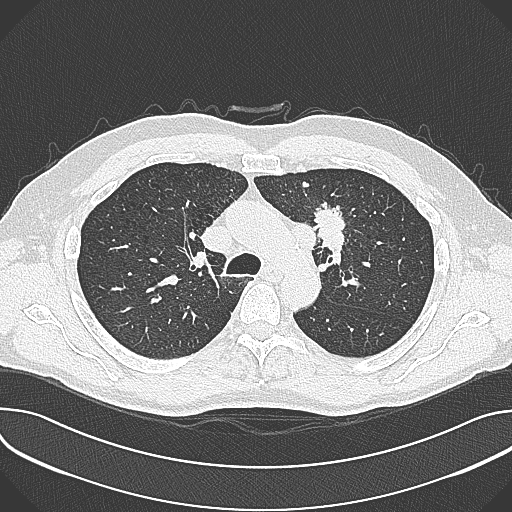
Axial slice from a low-dose chest CT screening exam. First (baseline) screen. Lung window (W 1500 / L -600 HU). 1 mm slice thickness. Male participant, aged 59 years at enrolment.
Expert reader's lesion annotation, bounding box [x1, y1, x2, y2] px = [302, 197, 361, 257]. The screening reader recorded 2 non-calcified nodules or masses ≥4 mm on this exam; which of them this box marks is not recorded. Official screen result: positive, change unspecified: nodule(s) >= 4 mm or enlarging nodule(s), mass(es), or other non-specific abnormalities suspicious for lung cancer. Later outcome: lung cancer diagnosed 21 days after this screen — non-small cell carcinoma, left upper lobe, poorly differentiated (G3), stage IIIA (AJCC 6th edition), 35 mm at pathology.